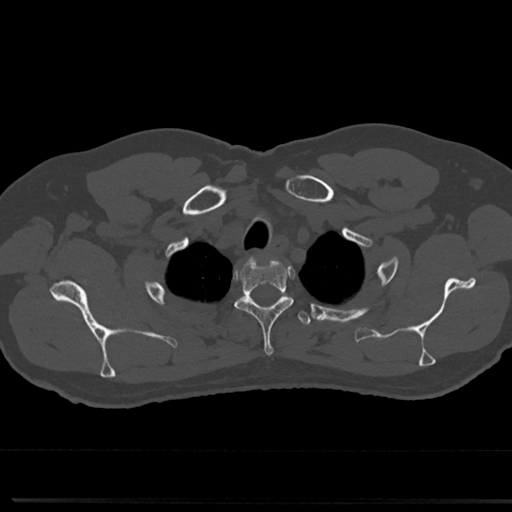
CT including the spine, one axial slice; reconstruction kernel Br40s/3; 120 kVp; bone window (W 1800 / L 400 HU); 0.5 mm slice thickness; 512 × 512 image matrix. Male patient, age 61 years. Case-level facts recorded for this patient, not image findings: primary cancer: prostate.
Annotated regions visible in this slice (semi-automatic segmentation, software-assisted and operator-edited):
- T1 vertebra: box from (x=241, y=298) to (x=285, y=302) px
- T2 vertebra: (x=235, y=253)–(x=293, y=357)
- T3 vertebra: (x=280, y=298)–(x=311, y=327)